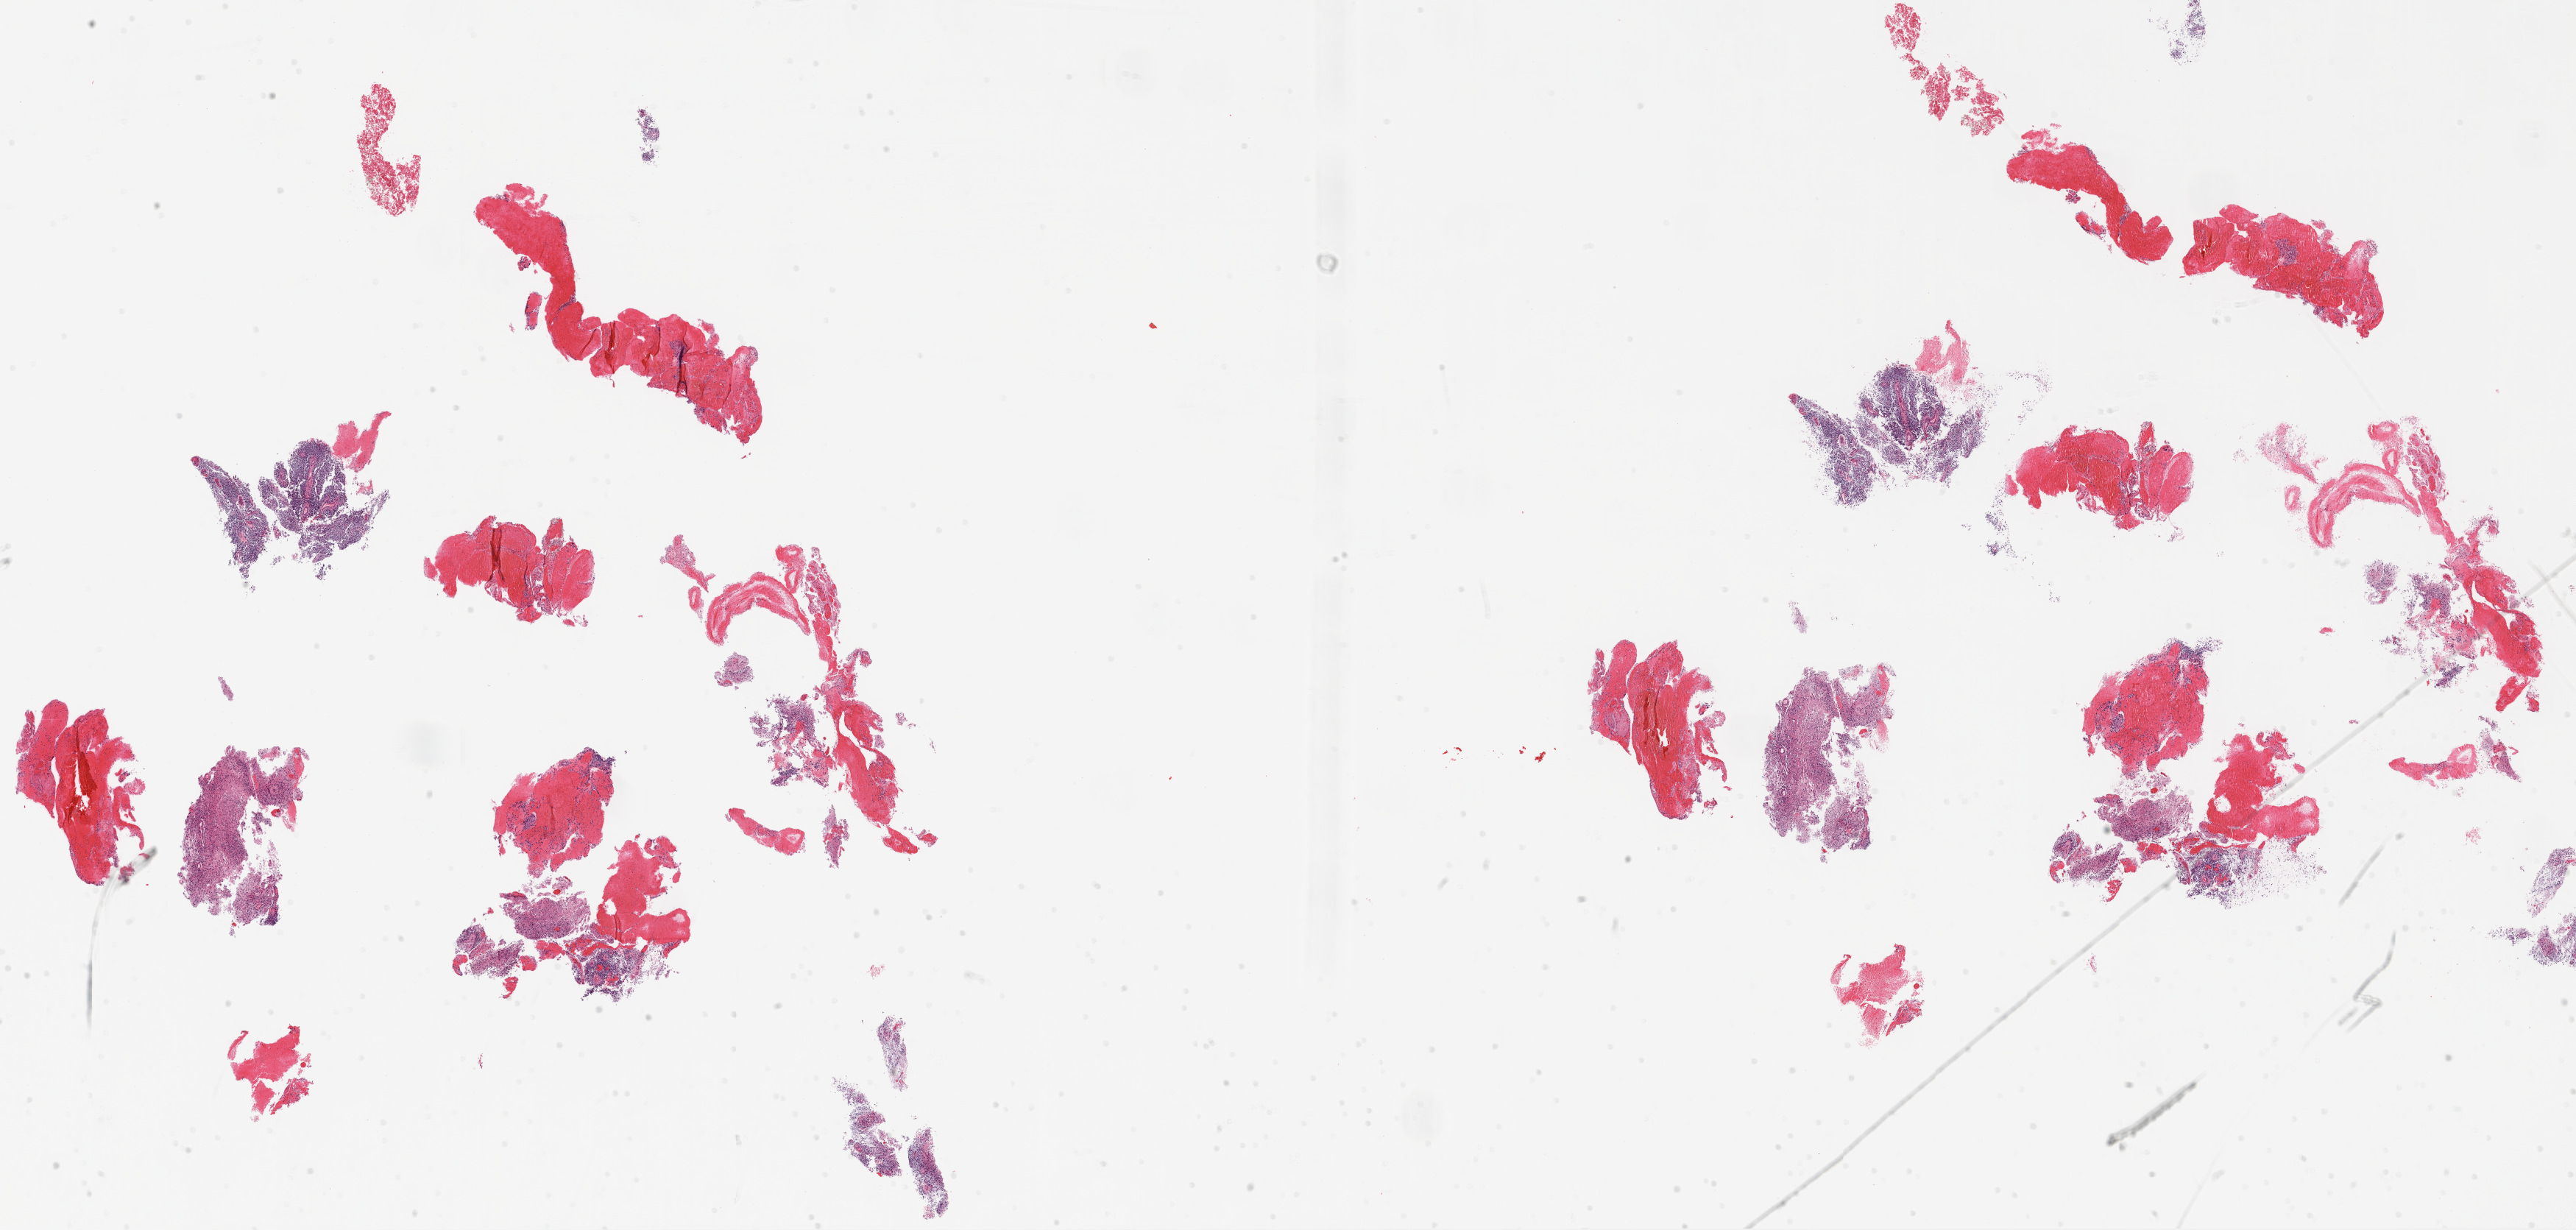
Hematoxylin and eosin (H&E) stained whole-slide image, shown as a low-resolution overview of the whole scanned area (about 28.1 x 13.4 mm, slide scanned at 20x), formalin-fixed paraffin-embedded (FFPE) diagnostic section, sample: primary tumour, brain. Patient: male, age at initial diagnosis 61 years.
Pathologic diagnosis: Glioblastoma.